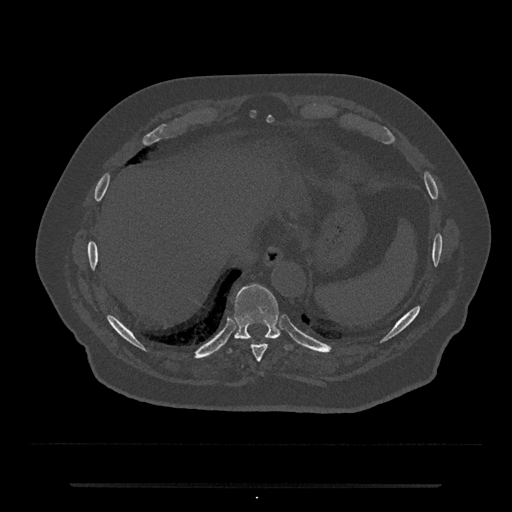
CT including the spine, one axial slice; slice 729 of 797 in the series (ordered by position); 120 kVp; bone window (W 1800 / L 400 HU); 0.5 mm slice thickness; 512 × 512 image matrix, field of view 434 × 434 mm. Patient: male, 80 years. Case-level facts recorded for this patient, not image findings: primary cancer: prostate; vertebrae with lytic lesions (as recorded): L1, T11.
Structures marked on this image (semi-automatic segmentation, software-assisted and operator-edited):
- T10 vertebra: box from (x=228, y=284) to (x=293, y=353) px
- T9 vertebra: (x=243, y=338)–(x=272, y=362)